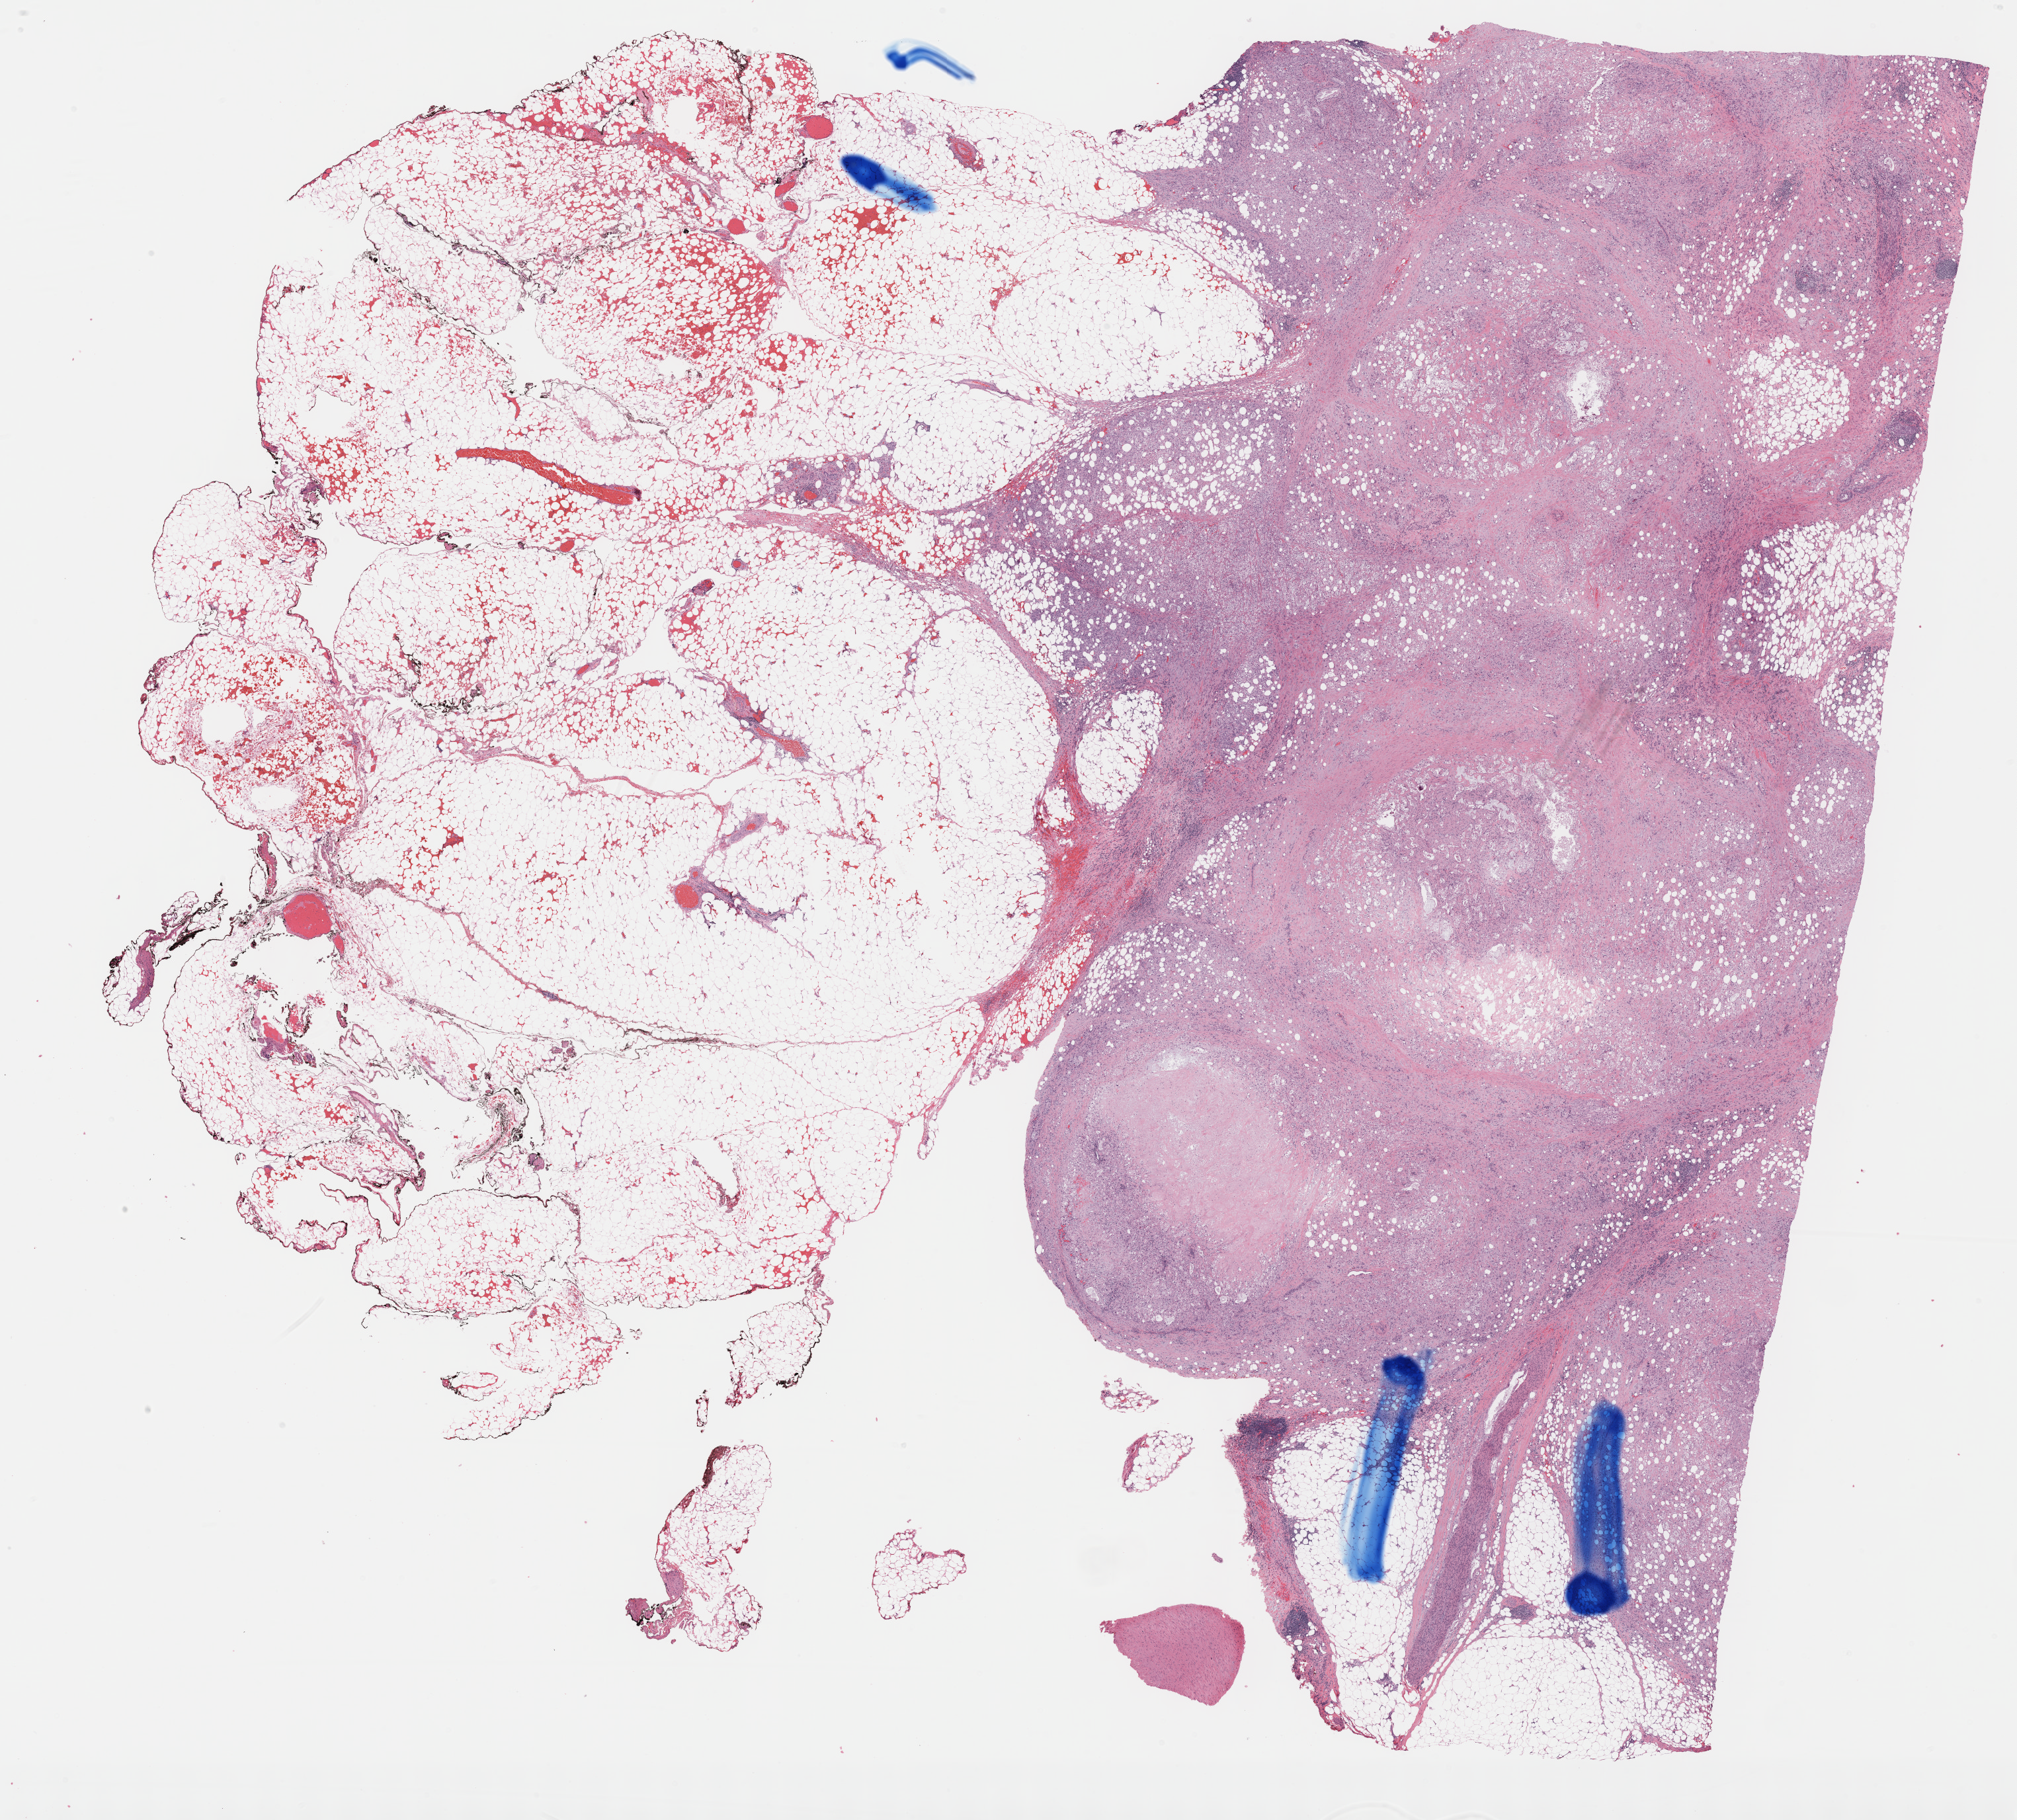
Digitized Hematoxylin and eosin (H&E) stained tissue section (whole slide) — shown as a low-resolution overview of the whole scanned area (about 24.7 x 22.3 mm, acquisition: 40x scan); formalin-fixed paraffin-embedded (FFPE) diagnostic section; pancreas, primary tumour sample. Patient: male, age at initial diagnosis 50 years. Histologic grade: G2 (moderately differentiated).
• pathologic diagnosis: Infiltrating duct carcinoma, NOS (tail of pancreas)
• lymph nodes positive (case pathology): 13 of 21 examined
• AJCC pathologic stage: IIB